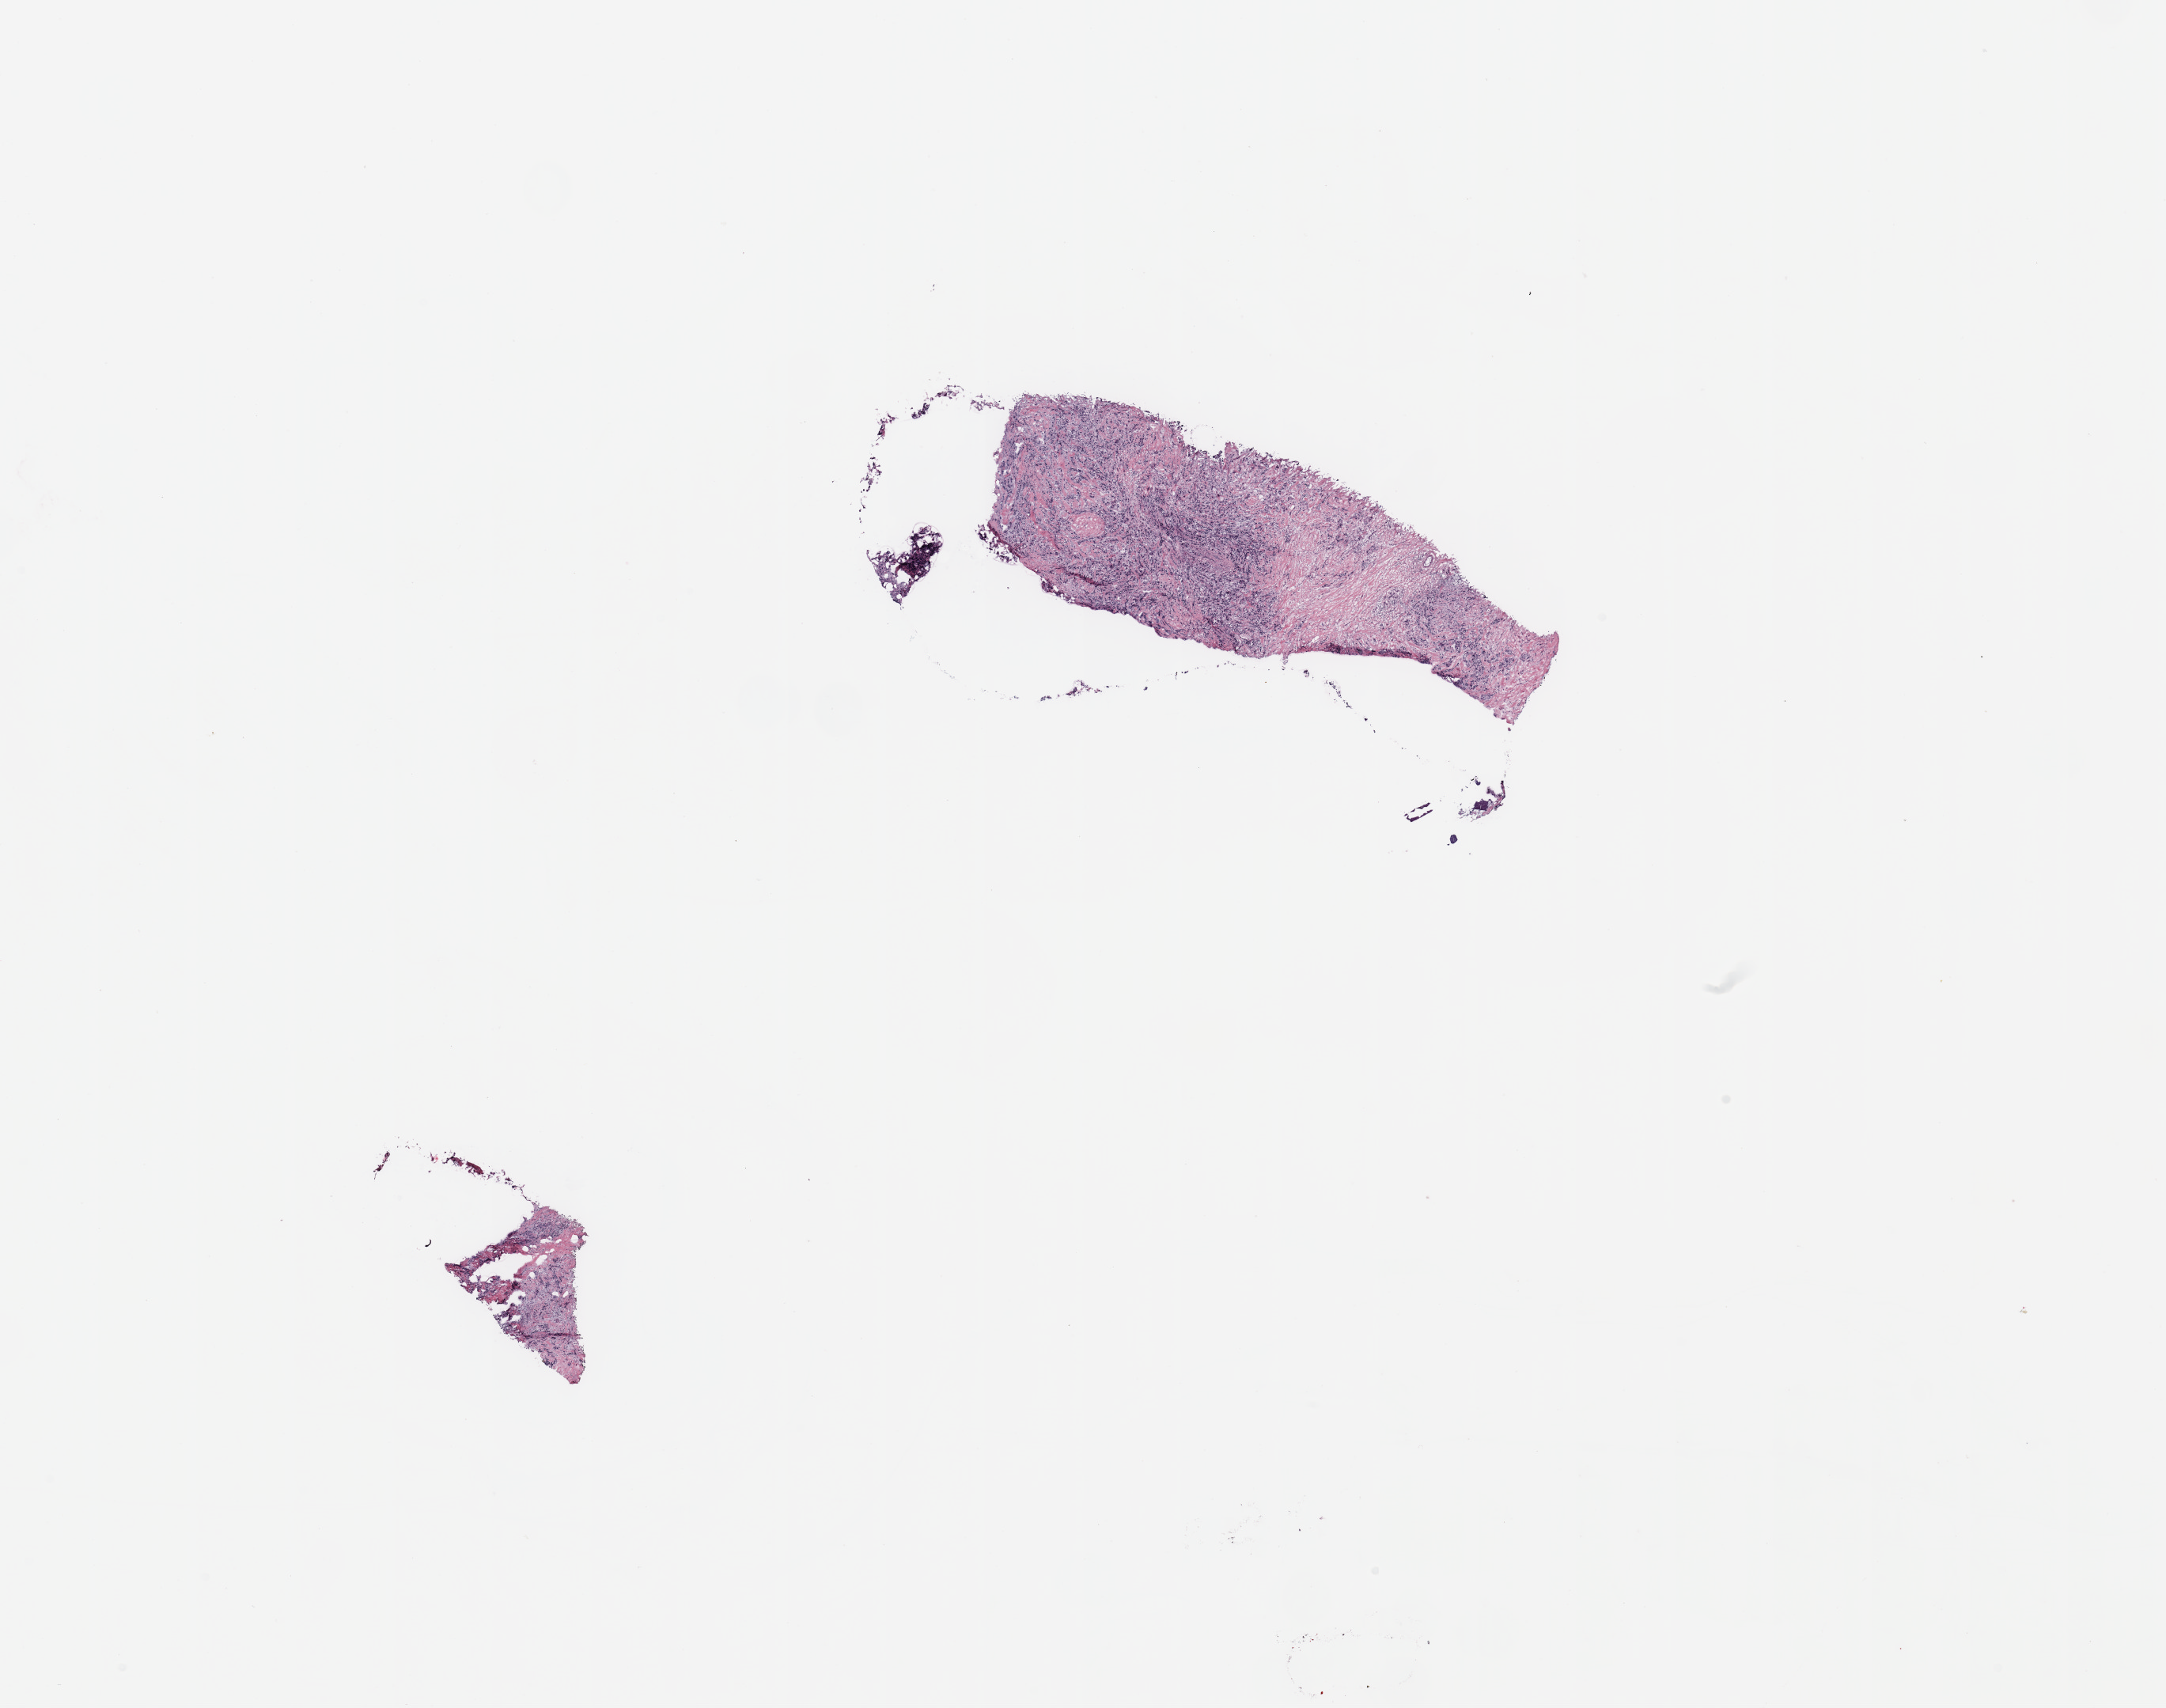
Hematoxylin and eosin (H&E) stained whole-slide image — a low-resolution overview of the entire scanned area, about 21.7 x 17.1 mm; breast, tissue type not recorded.
• patient diagnosis (cohort enrolment): breast cancer (breast)